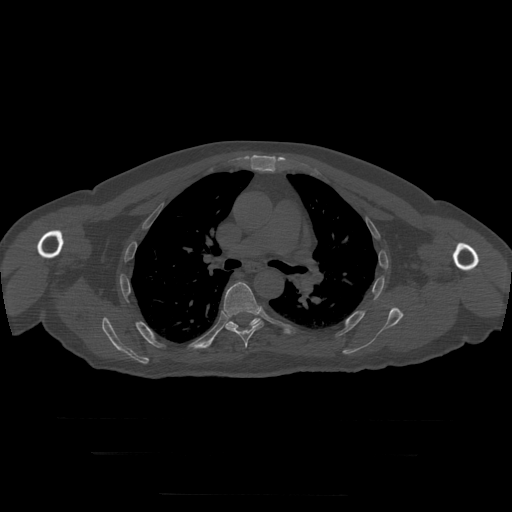
CT including the spine, one axial slice; slice 201 of 397 in the series (ordered by position); bone window (W 1800 / L 400 HU); 1.25 mm slice thickness; 512 × 512 image matrix, field of view 510 × 510 mm. Patient age 73 years. Case-level facts recorded for this patient, not image findings: primary cancer: prostate.
Structures marked on this image (semi-automatic segmentation, software-assisted and operator-edited):
- T6 vertebra: box from (x=223, y=282) to (x=264, y=348) px
- T7 vertebra: (x=227, y=318)–(x=262, y=328)